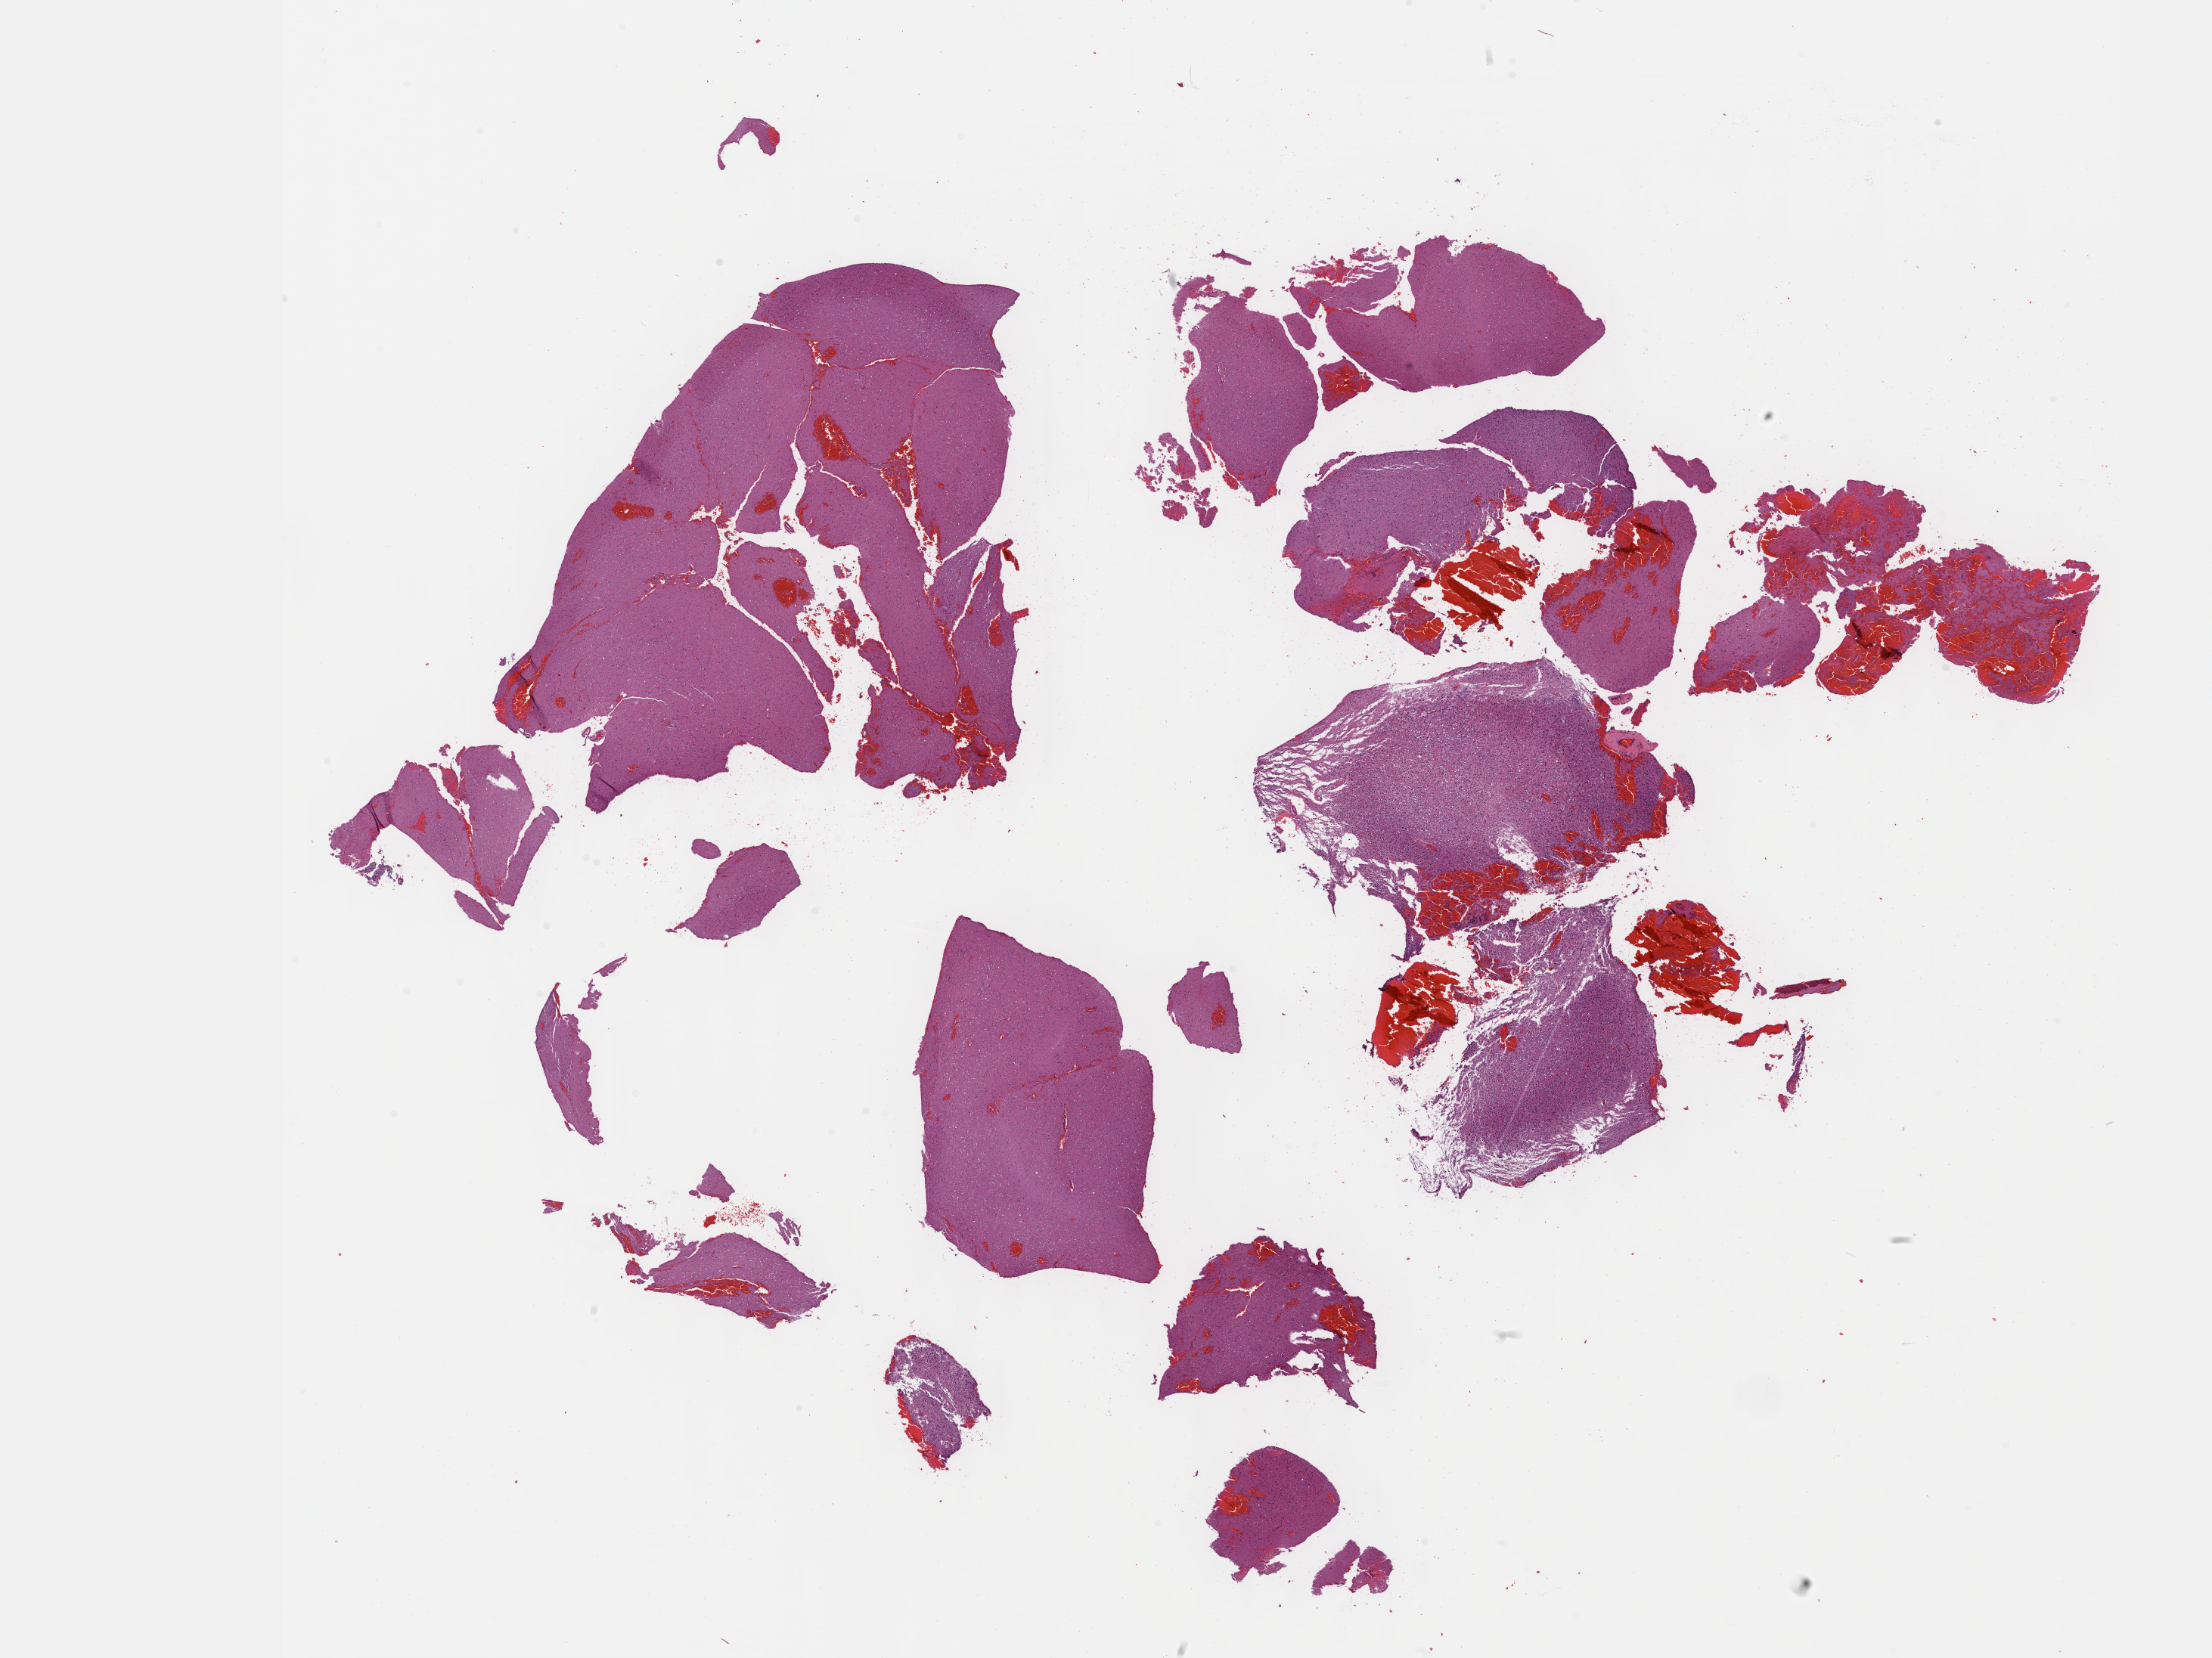
Digitized H&E tissue section (whole slide) — a low-resolution overview of the entire scanned area, about 23.6 x 17.7 mm (acquisition: 40x scan), formalin-fixed paraffin-embedded (FFPE) diagnostic section, brain, primary tumour sample. Patient: male, age at initial diagnosis 31 years. Histologic grade: G3 (poorly differentiated).
• diagnosis: Mixed glioma (cerebrum)